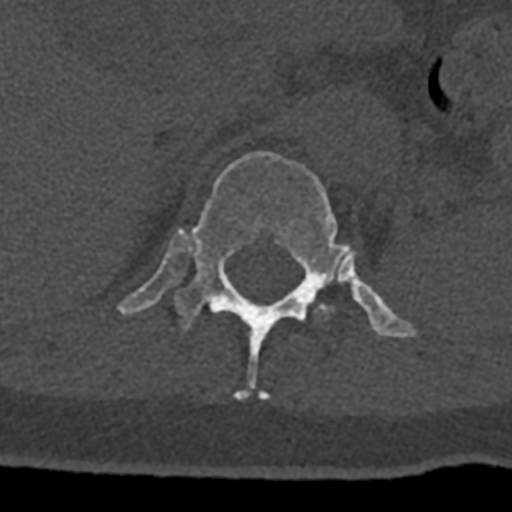
CT including the spine, one axial slice. Position 494 of 797 along the scan axis. 120 kVp. Bone window (W 1800 / L 400 HU). 0.5 mm slice thickness. 512 × 512 image matrix. Patient: male, 74 years. Case-level facts recorded for this patient, not image findings: primary cancer: renal; vertebrae with lytic lesions (as recorded): T10, L1, L2, L3, L4, L5.
Annotated regions visible in this slice (semi-automatically segmented with operator editing):
- L1 vertebra: bounding box (x1, y1, x2, y2) in pixels: (315, 305, 326, 313)
- T12 vertebra: (117, 151, 417, 400)